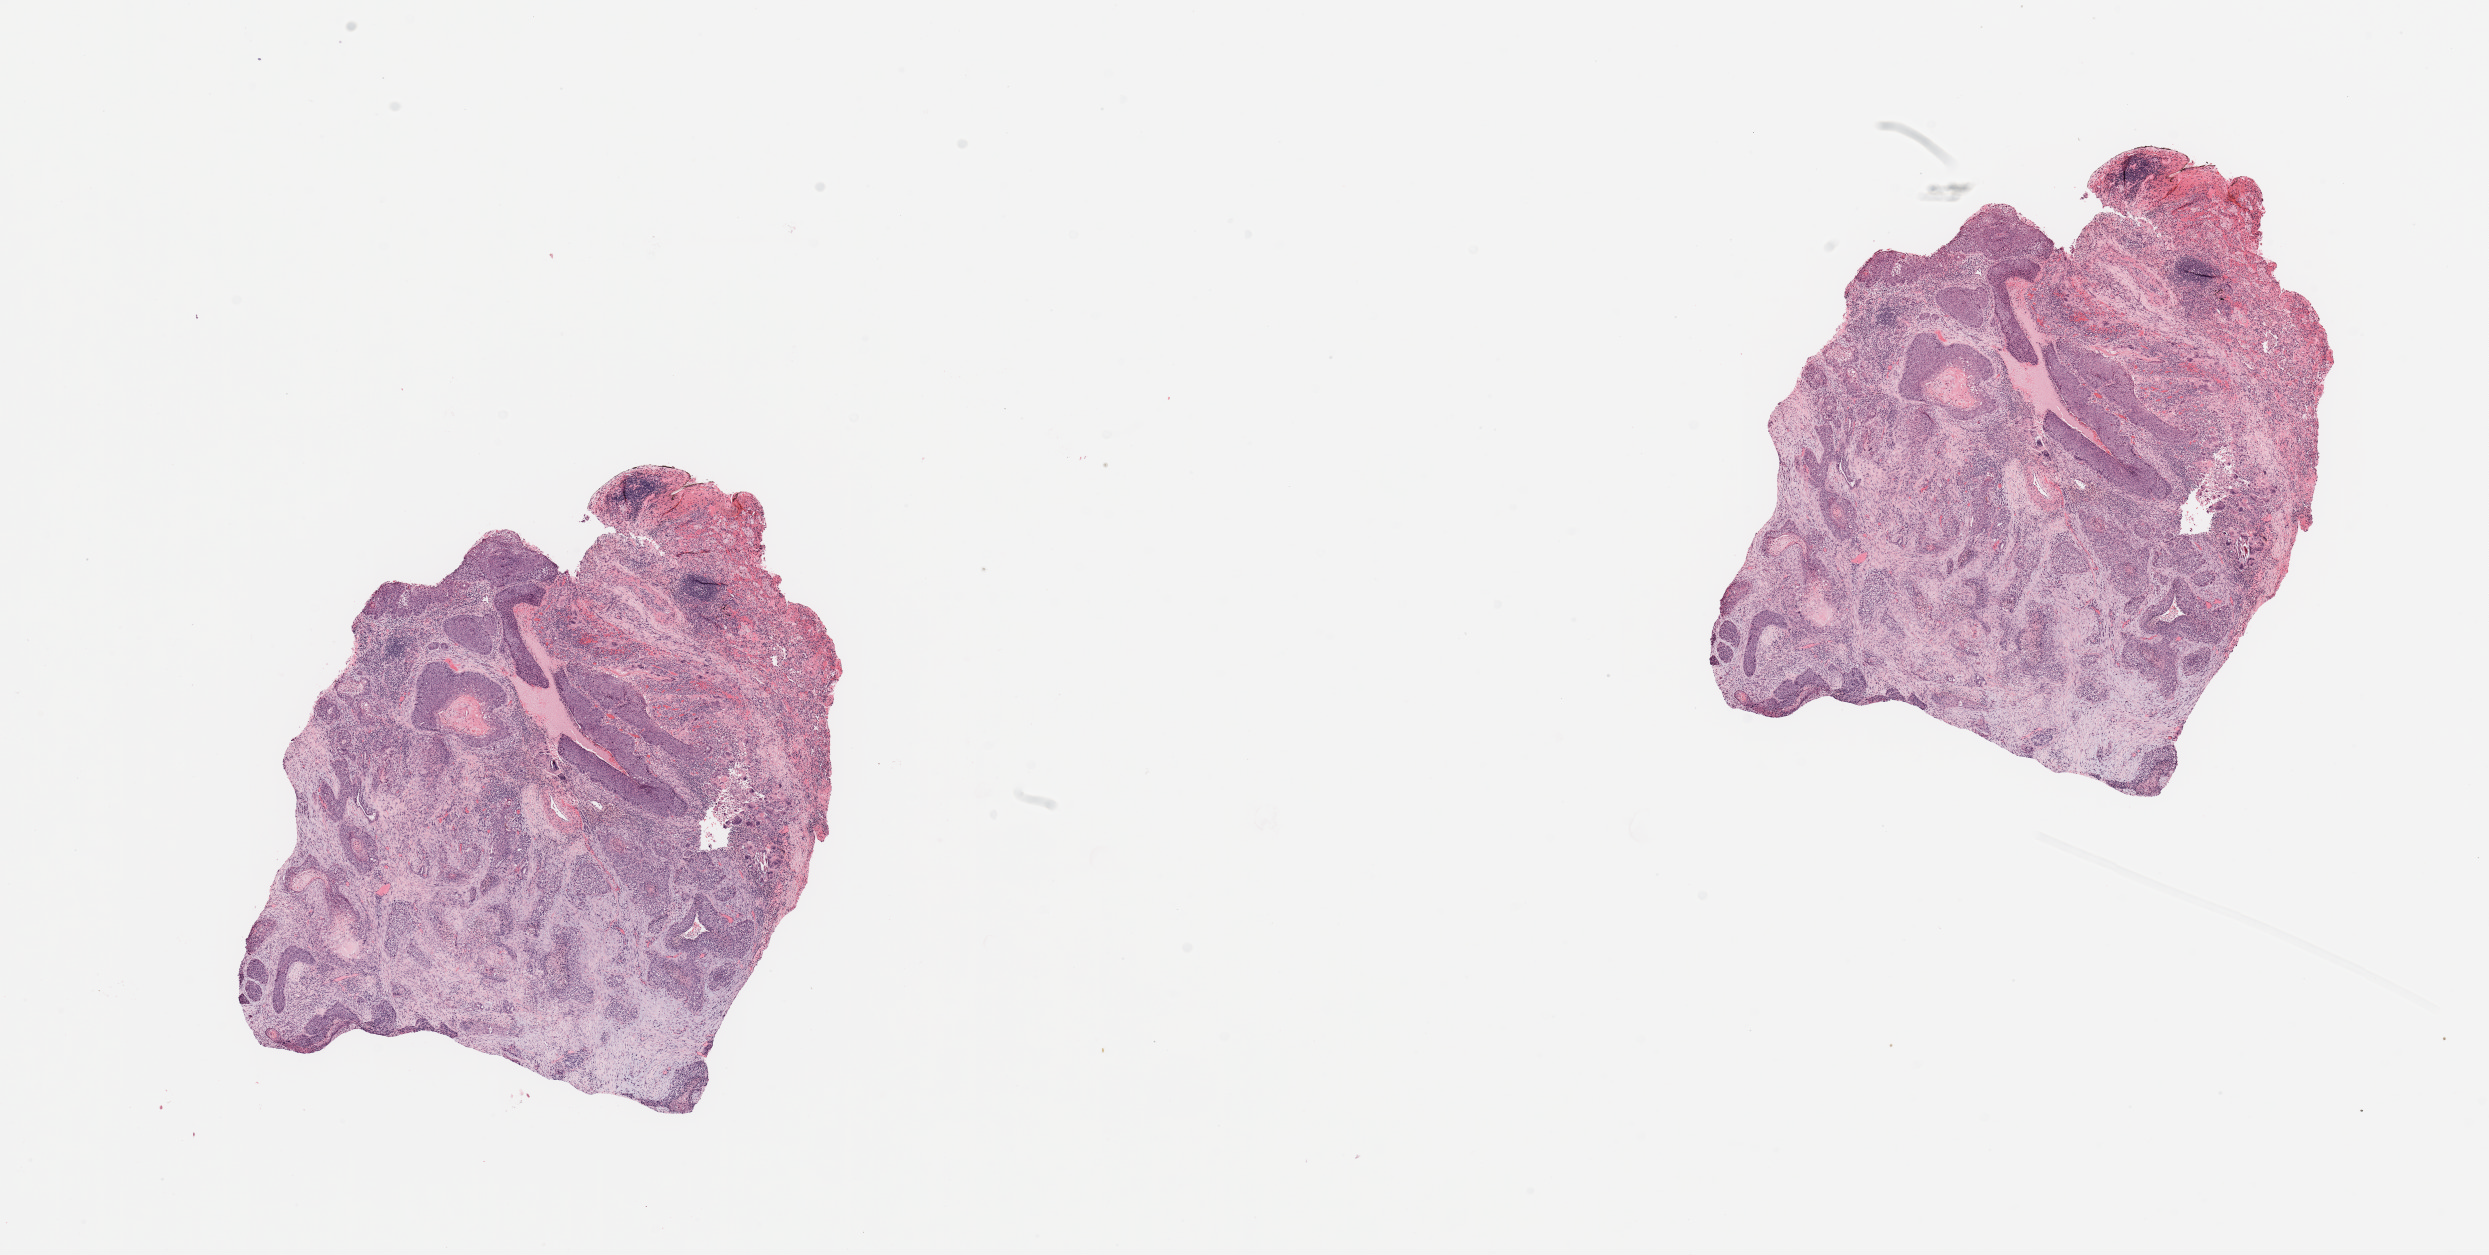
H&E whole-slide image, a low-resolution overview of the entire scanned area, about 19.7 x 9.9 mm; tumour tissue sample, sampled site: lung. 61-year-old male patient. Histologic grade: G2 (moderately differentiated). Slide review estimates, as recorded: tumour nuclei 60%, necrosis 10%.
• AJCC pathologic stage: IA
• histologic diagnosis: Squamous cell carcinoma, NOS
• primary tumour site (as recorded): left lower lobe